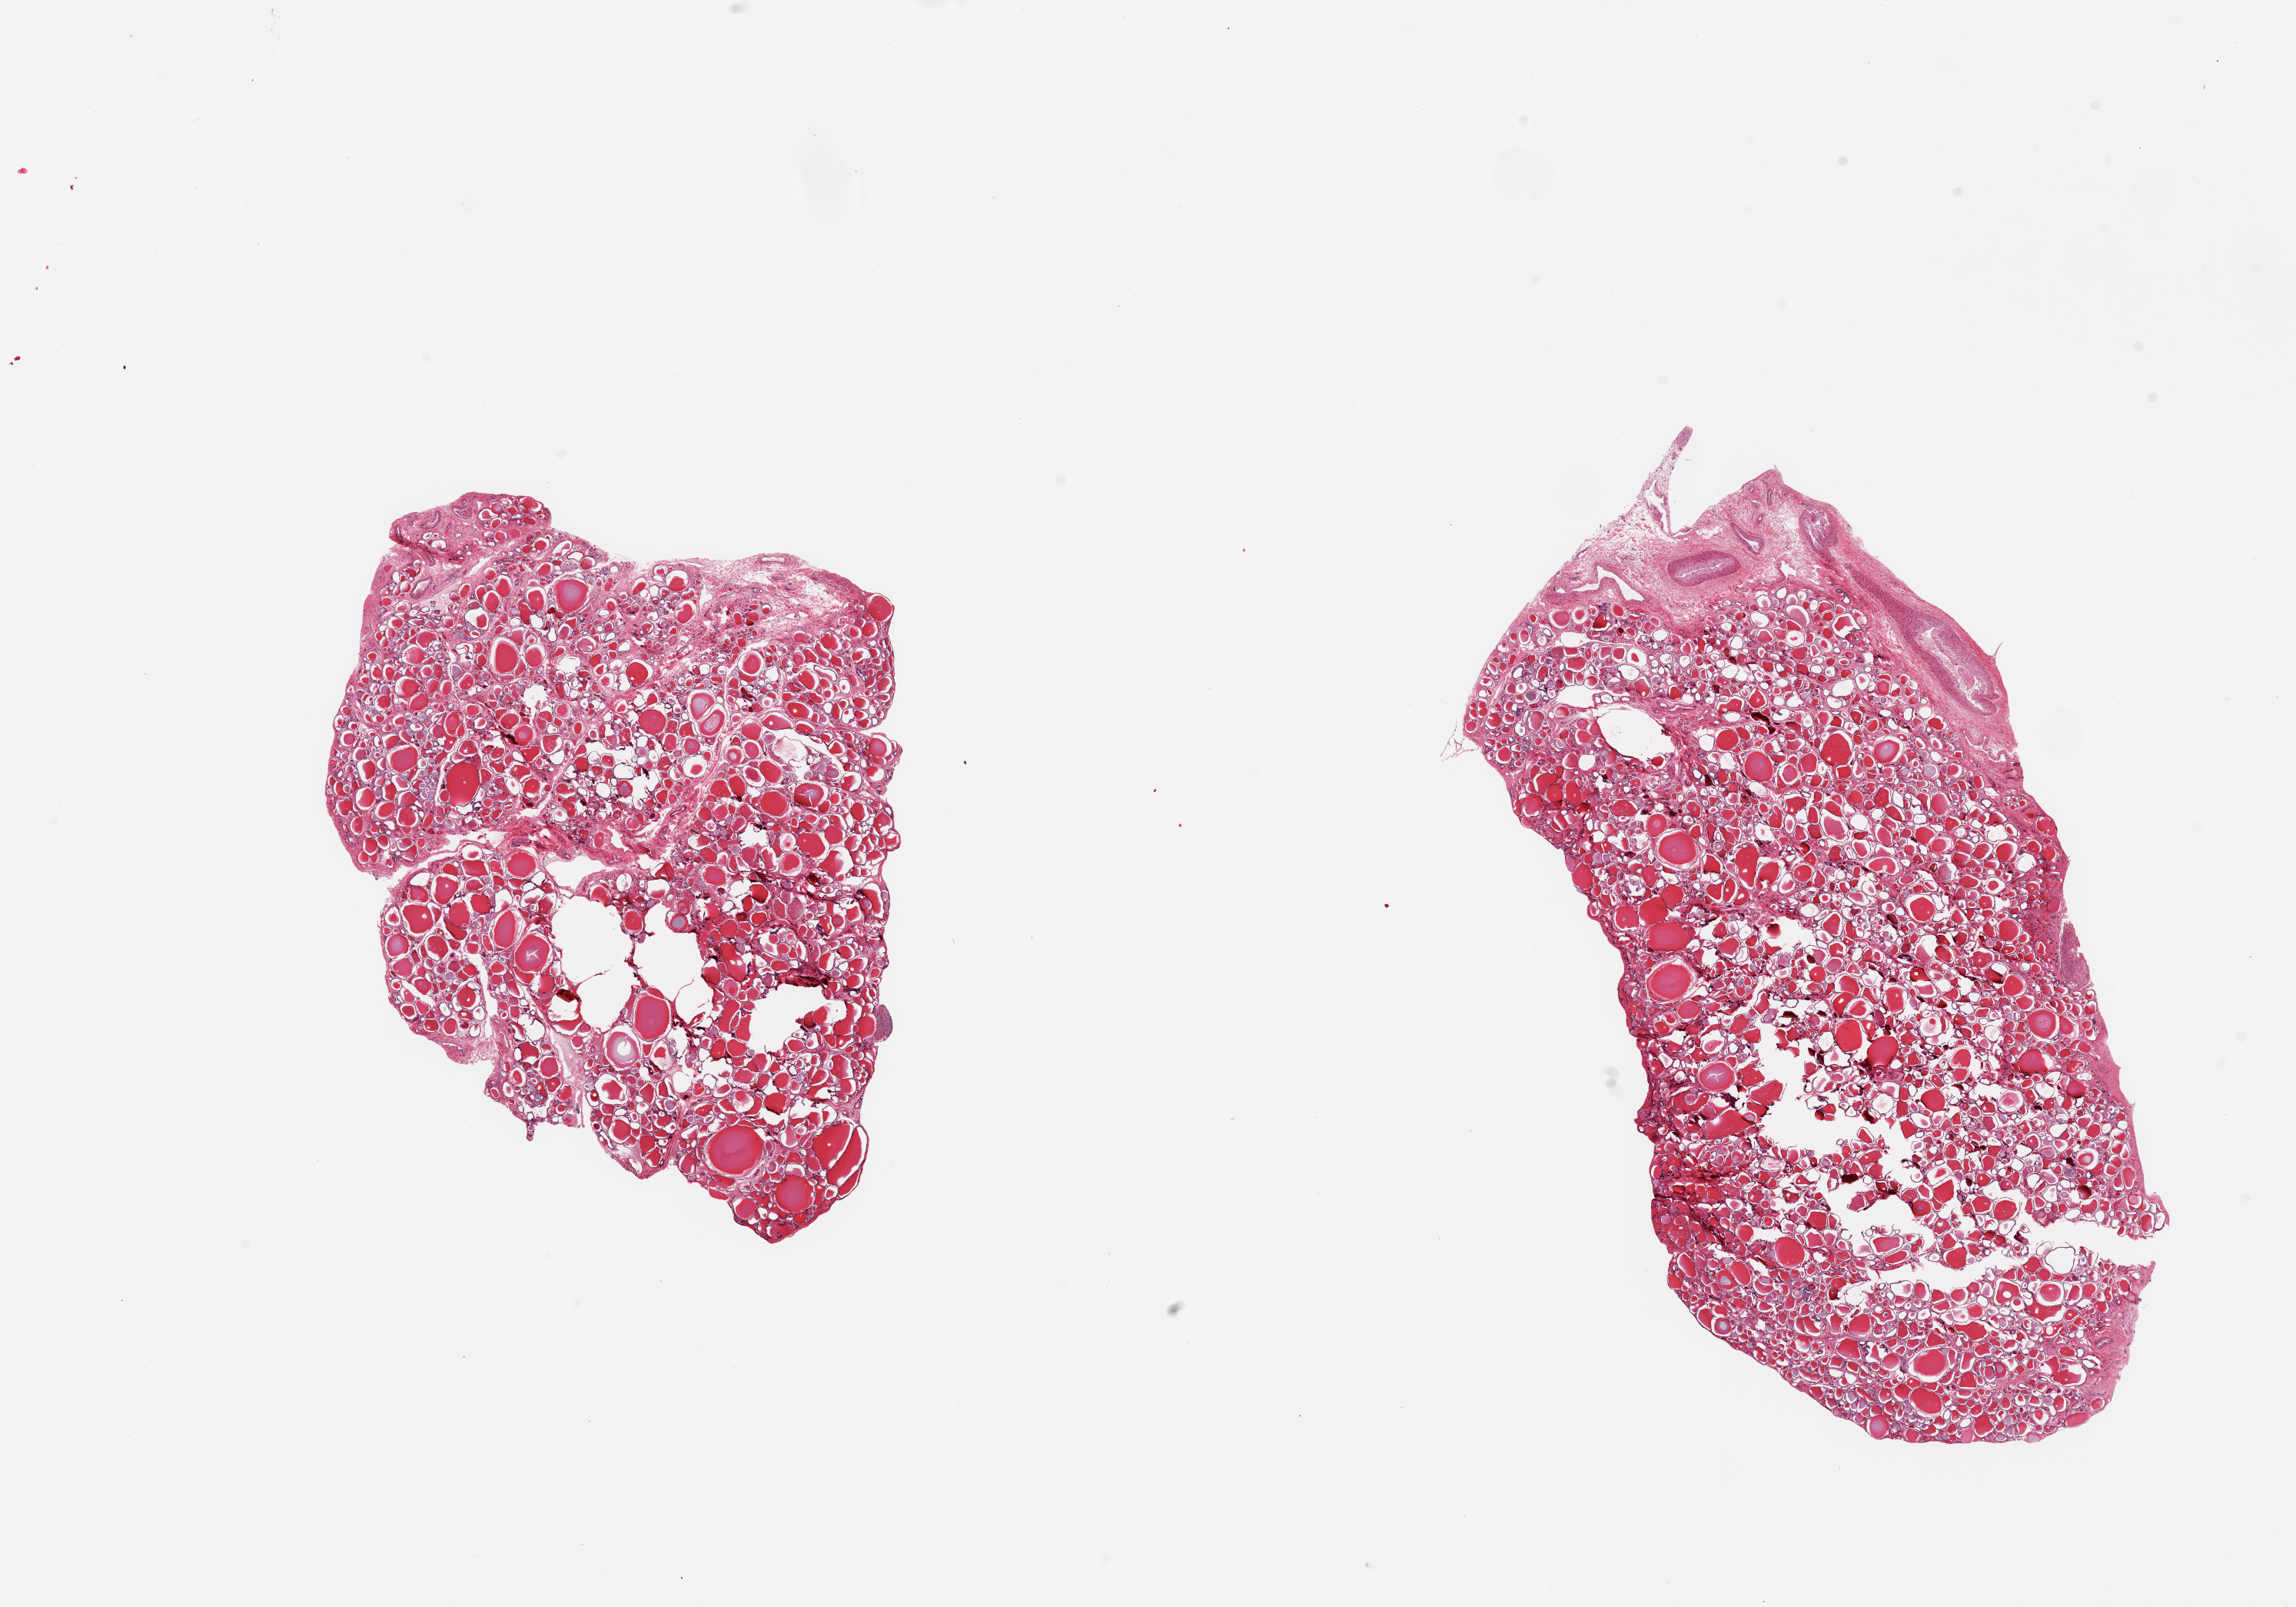
Digitized H&E-stained section — a low-resolution overview of the entire scanned area, about 23.6 x 16.5 mm (acquisition: 20x scan); PAXgene-fixed, paraffin-embedded tissue; sampled site (target tissue): thyroid; donor tissue sample. Donor: female.
* reviewer comment on this tissue sample: 2 pieces, no abnormalities; 1mm nubbin of fibrovascular tissue